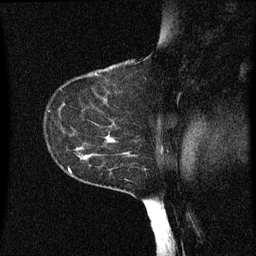
Breast MRI (dynamic contrast-enhanced), one sagittal slice. Position 44 of 60 along the scan axis. Dynamic contrast-enhanced series, image 2 of 3 at this slice position (ordered by acquisition). 1.5 T. TE 4.2 ms, TR 8 ms. 256 × 256 image matrix. Female patient, age 55 years.
Outlined on this slice (semi-automatic segmentation, software-assisted and operator-edited):
- analysis volume of interest (the breast-tissue region the enhancement analysis was run in; not a lesion): box from (x=46, y=124) to (x=151, y=183) px
- tumour enhancement mask (voxels above the 70 % enhancement threshold inside the analysis volume of interest): (x=76, y=134)–(x=115, y=149)